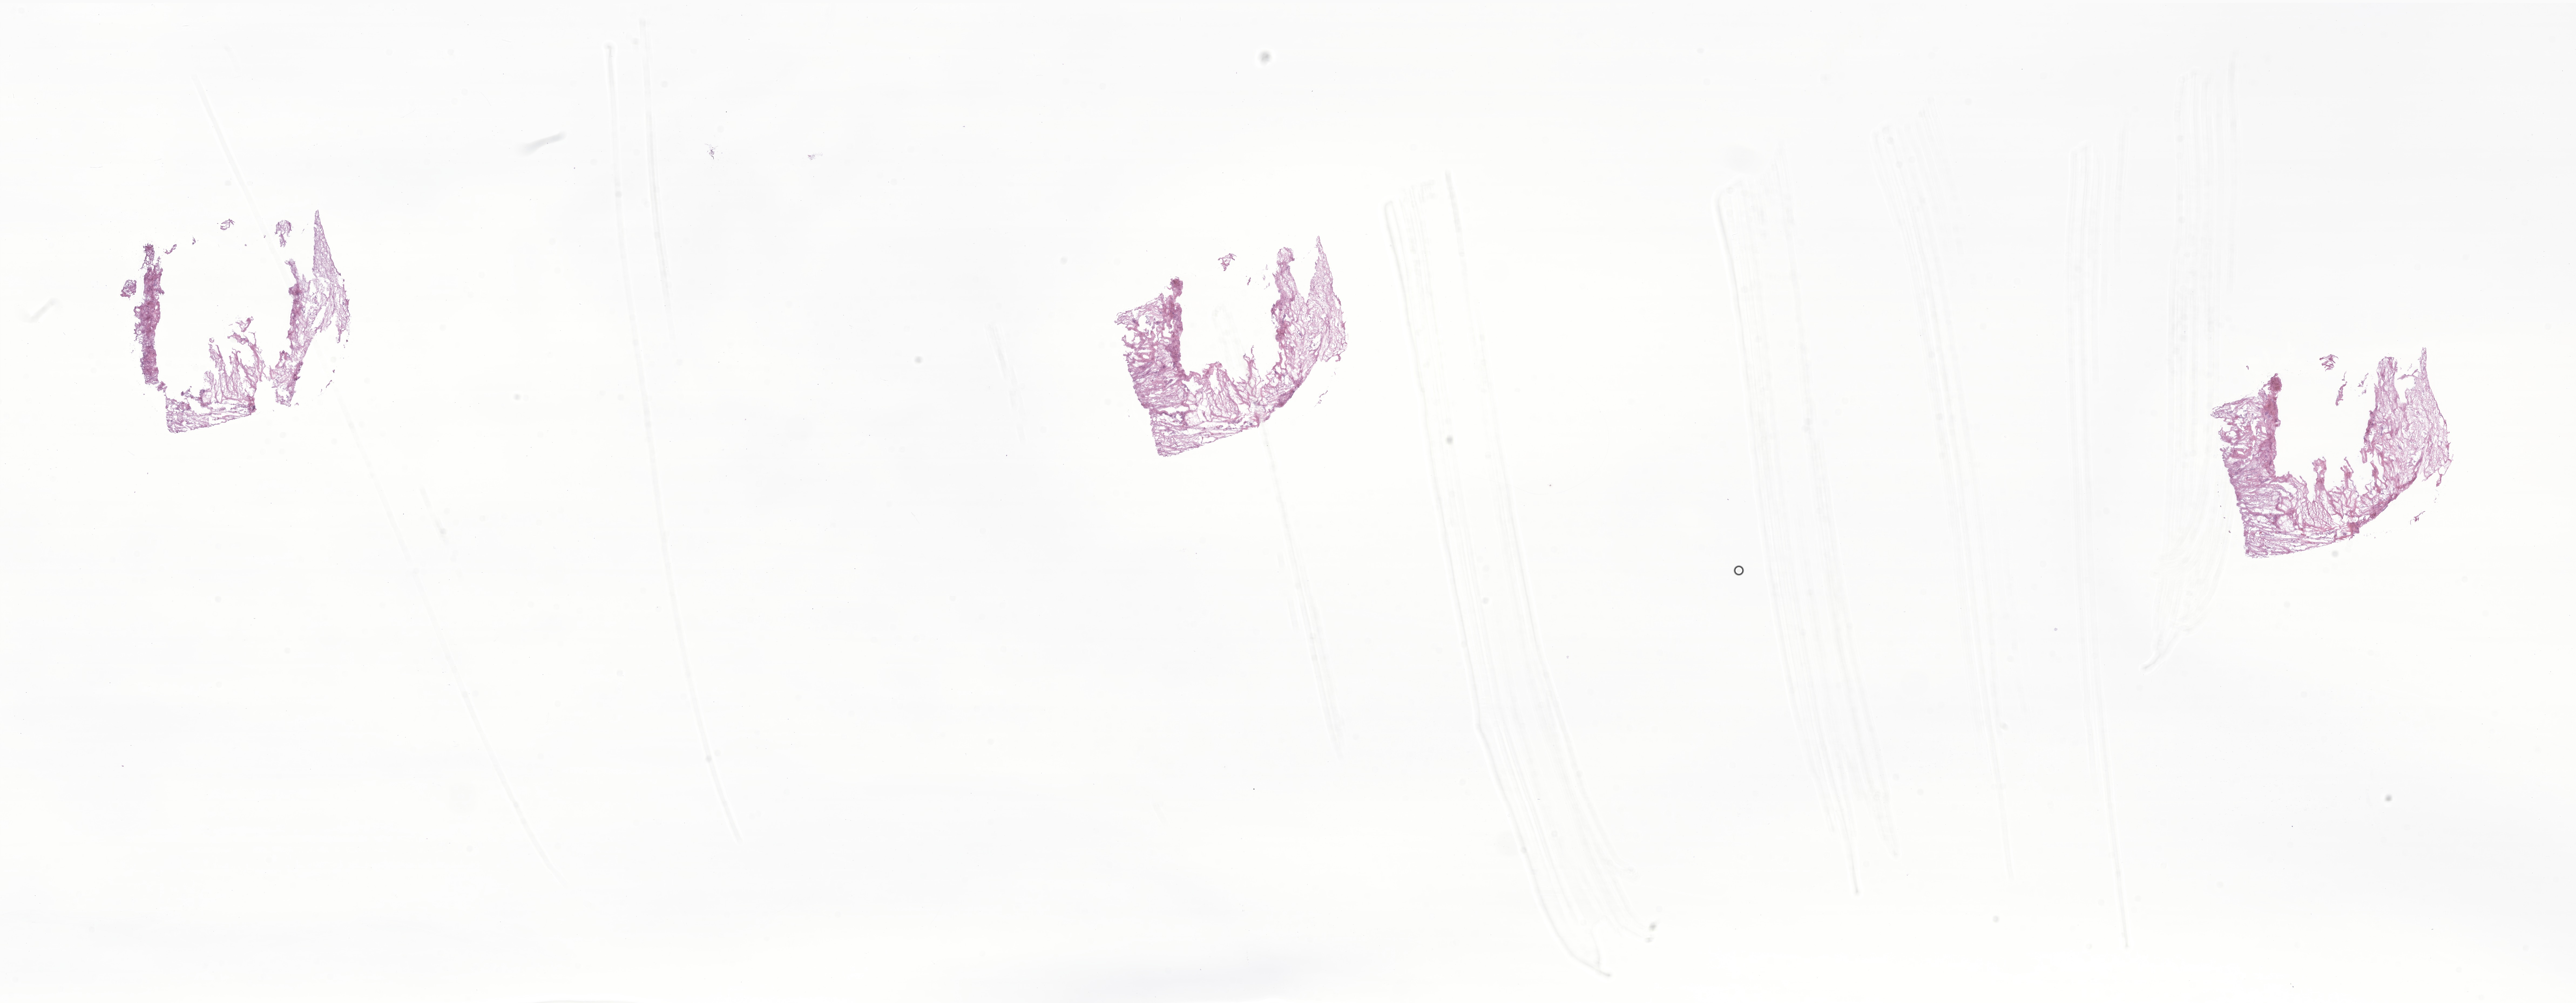
Digitized H&E-stained section of tumor tissue from the mandible, whole scanned area (about 40.2 x 15.7 mm) shown as a low-resolution overview. Frozen section. Female patient, age 53 months (4 years 5 months).
• diagnosis: Sarcoma, NOS